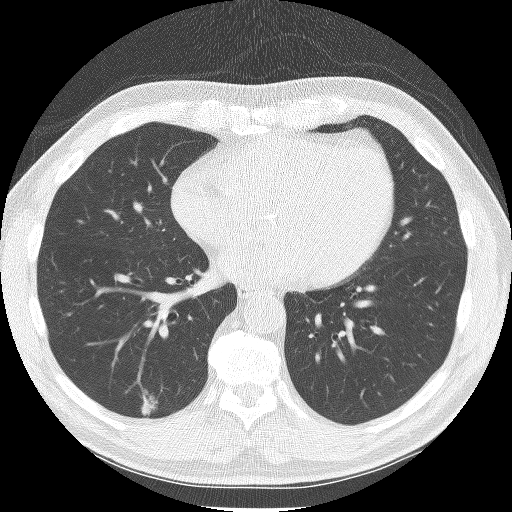
Chest CT (low-dose screening protocol), one axial image. Baseline annual screen. Lung window (W 1500 / L -600 HU). 2.5 mm slice thickness. Lung (sharp) reconstruction kernel (BONE). Slice 89 of 150 in the series. 512 × 512 image matrix, field of view 335 × 335 mm. Male participant, aged 61 years at enrolment. Current smoker at enrolment.
- Expert reader's lesion annotation, bounding box <125,384,167,424> (left, top, right, bottom; pixels).
- The exam's reader record, not a measurement of the box and not confirmed to be the same lesion: non-calcified nodule or mass ≥4 mm, right lower lobe, 12 × 11 mm, spiculated (stellate) margins, soft tissue attenuation.
- Official screen result: positive, change unspecified: nodule(s) >= 4 mm or enlarging nodule(s), mass(es), or other non-specific abnormalities suspicious for lung cancer.
- Later outcome: lung cancer diagnosed 232 days after this screen — adenocarcinoma, NOS, right lower lobe, moderately differentiated (G2), stage IA (AJCC 6th edition), 9 mm at pathology.